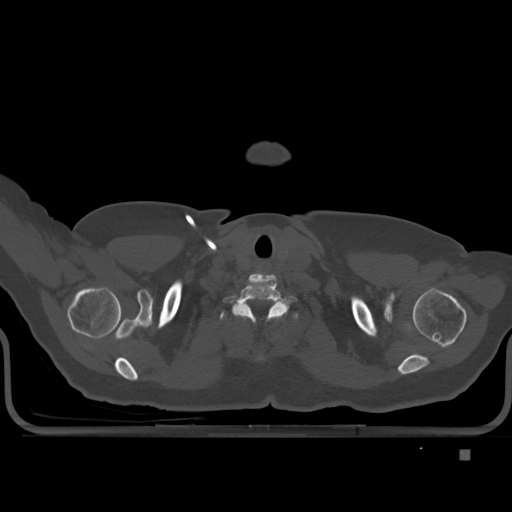
CT including the spine, one axial slice; bone window (W 1800 / L 400 HU); 512 × 512 image matrix, field of view 422 × 422 mm. Patient: female, 74 years. Case-level facts recorded for this patient, not image findings: primary cancer: colon.
Outlined on this slice (semi-automatic segmentation, software-assisted and operator-edited):
- T1 vertebra: box from (x=232, y=306) to (x=288, y=358) px